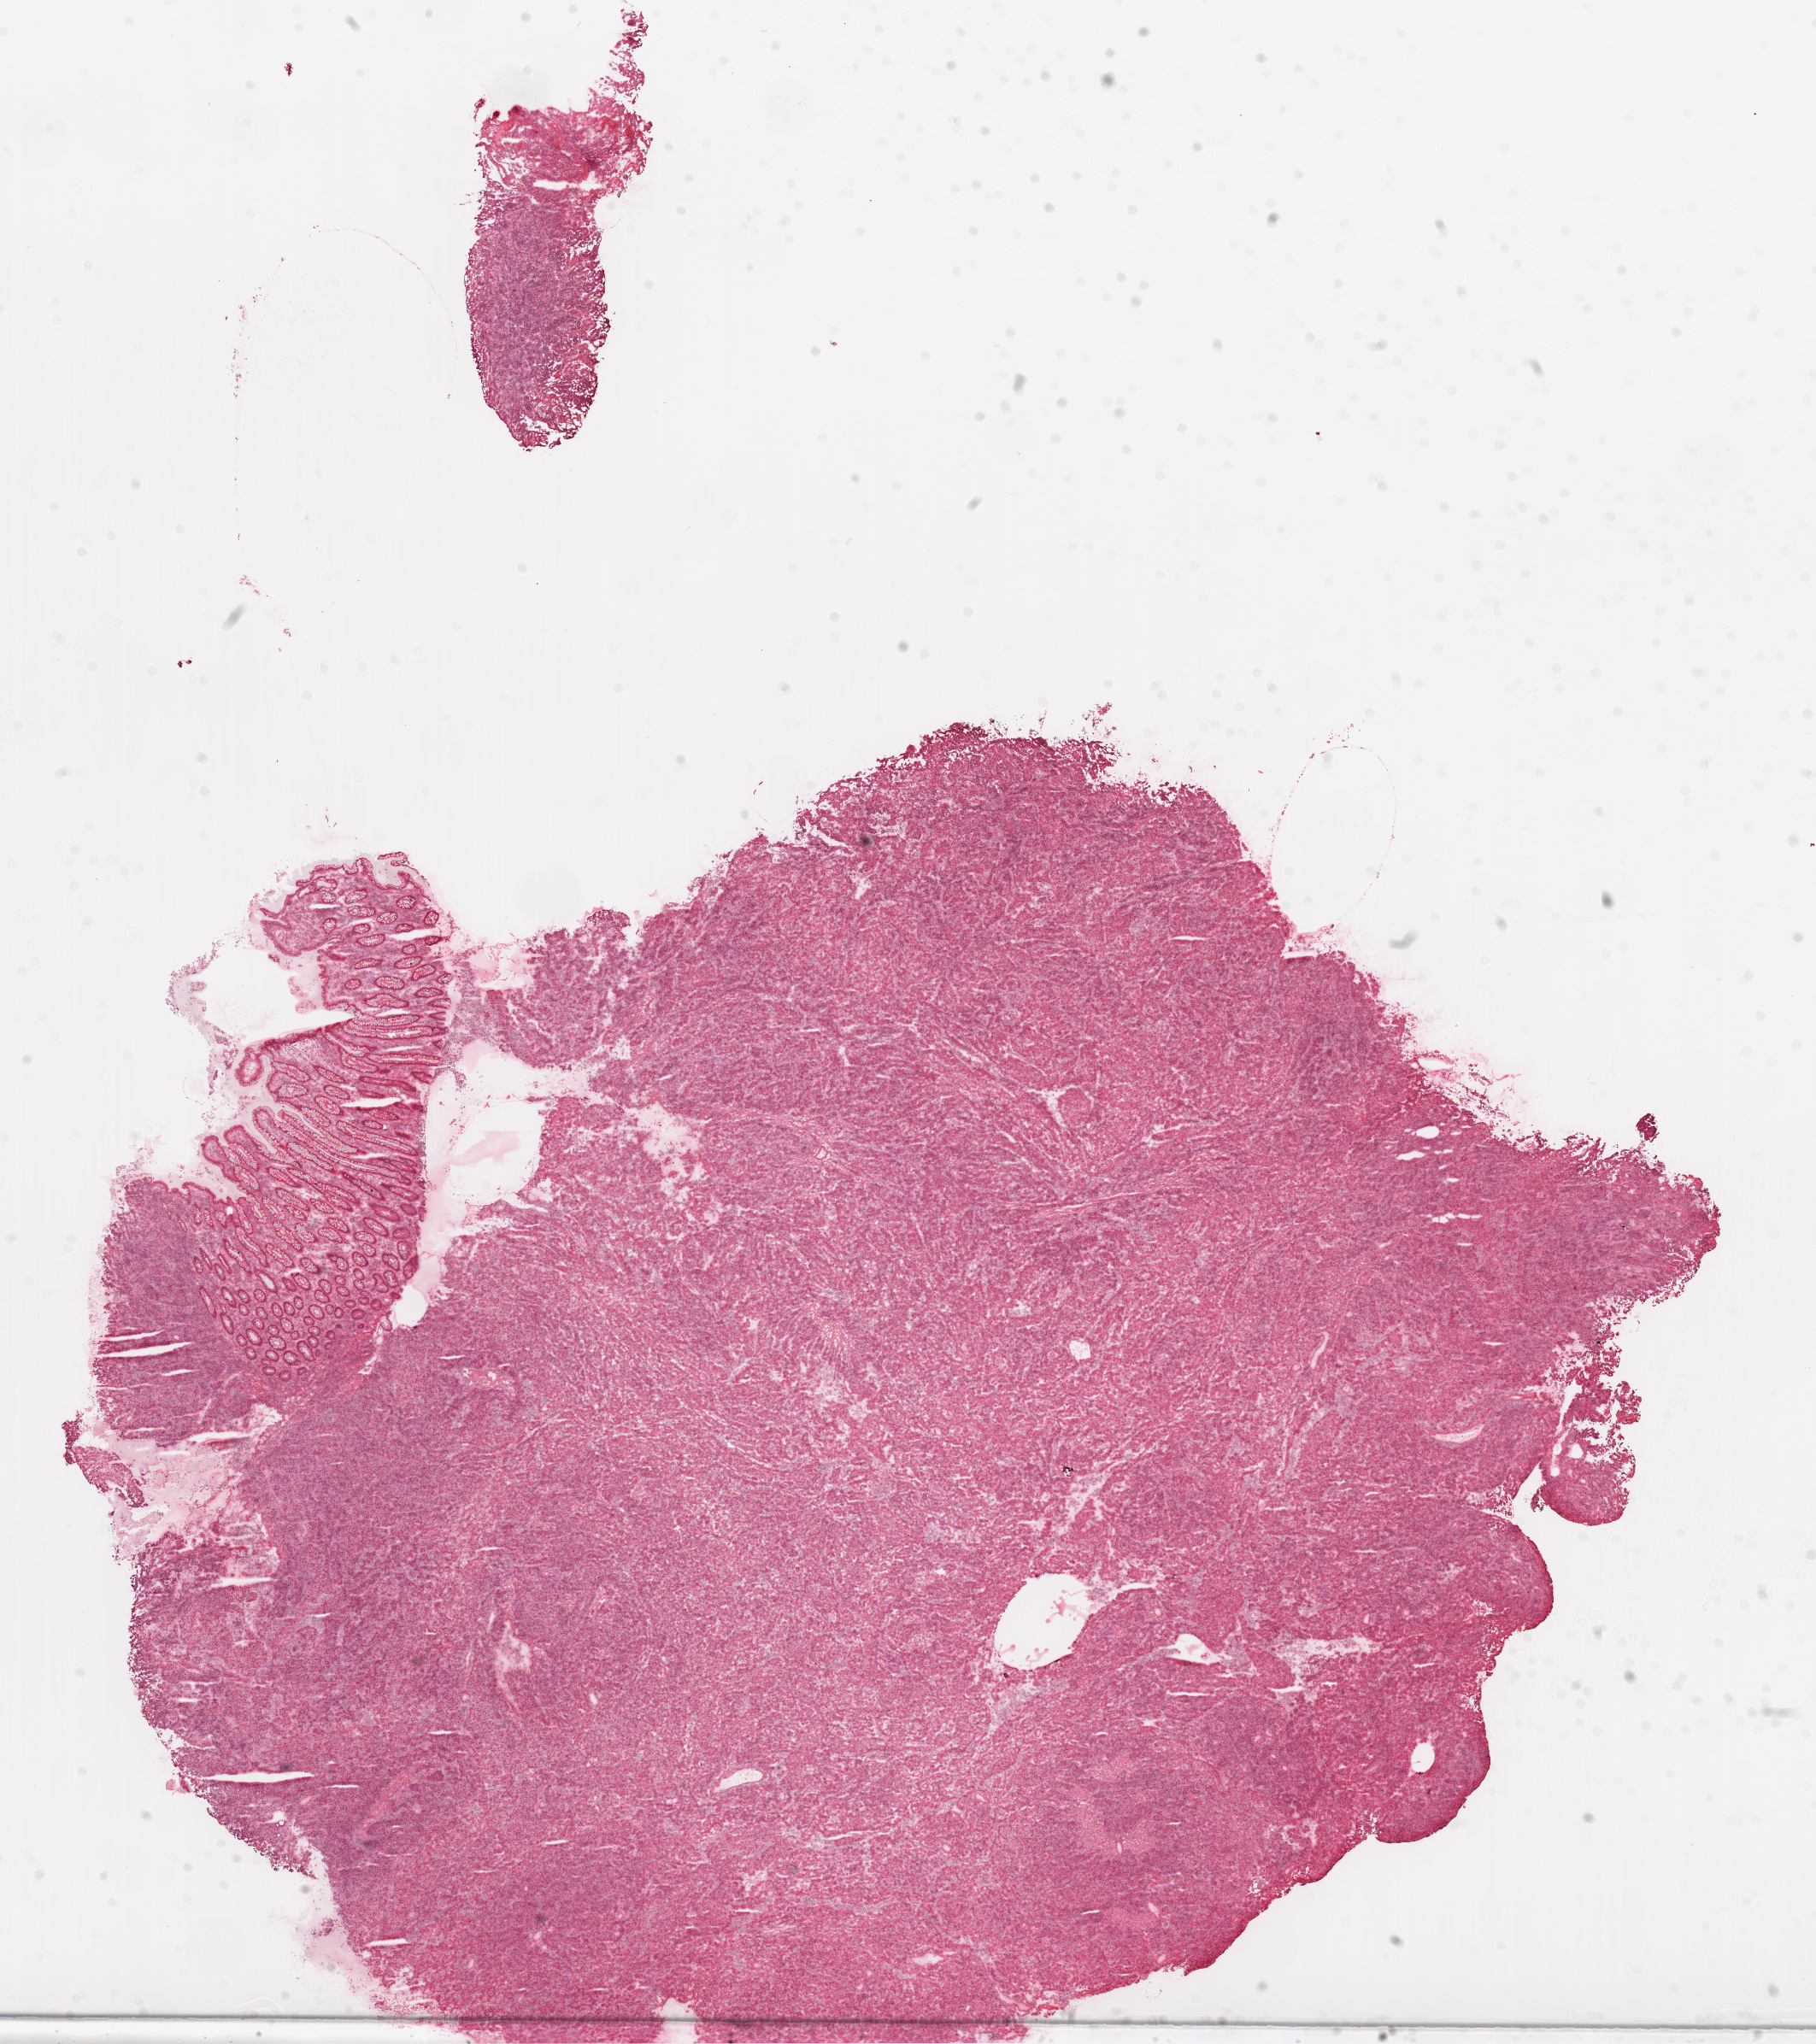
Digitized Hematoxylin and eosin (H&E) stained tissue section (whole slide), low-resolution overview of the scanned area, about 17.1 x 19.2 mm (slide scanned at 20x); frozen section from the top of the tissue portion; sample: primary tumour, colon. Patient: male, age at initial diagnosis 69 years. Composition of this section per pathologist review: tumour cells 90%, tumour nuclei 70%.
Pathologic diagnosis: Adenocarcinoma, NOS.